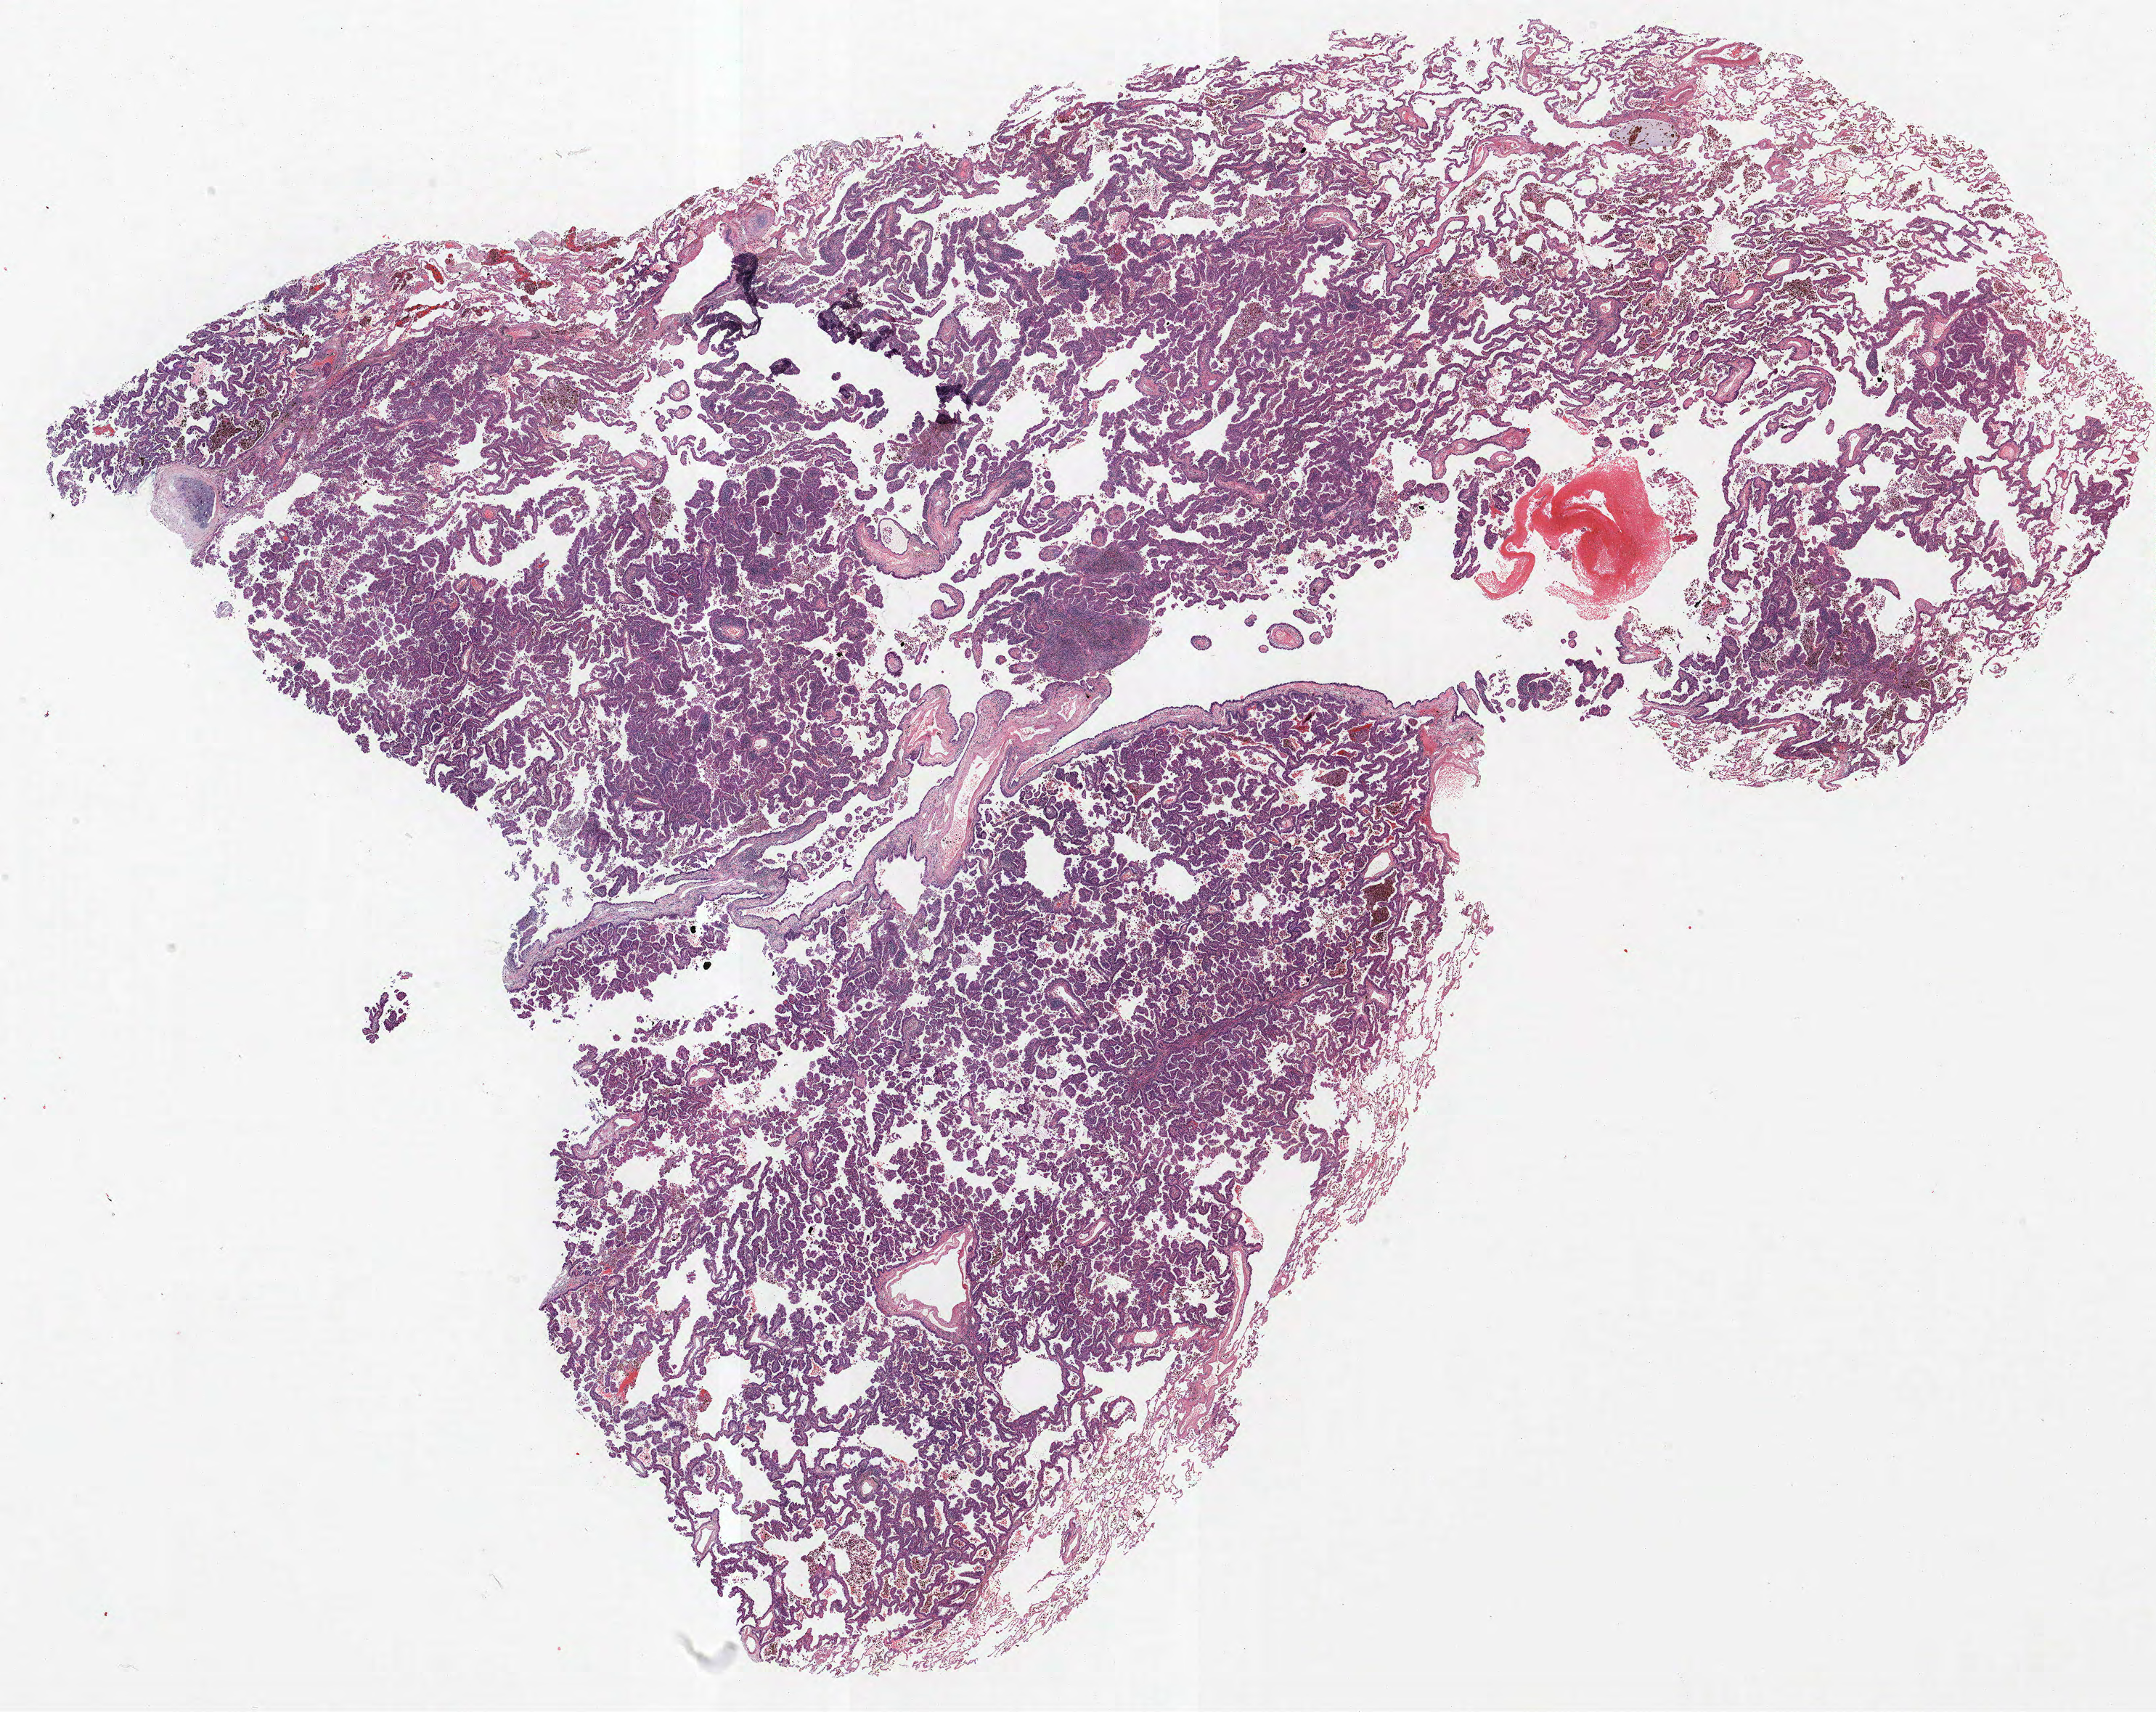
Whole-slide histology image, Hematoxylin and eosin (H&E) stained — shown as a low-resolution overview of the whole scanned area (about 23.8 x 18.9 mm, from a 40x scan), formalin-fixed paraffin-embedded (FFPE) section, lung tissue. Male patient, aged 60 at enrolment. Former smoker at enrolment. Grade: moderately differentiated (G2).
Tumour size (pathology): 32 mm. Primary tumour location (clinical record): right upper lobe. Participant's lung-cancer diagnosis: Papillary adenocarcinoma, NOS. Stage (AJCC 6th edition): IB.